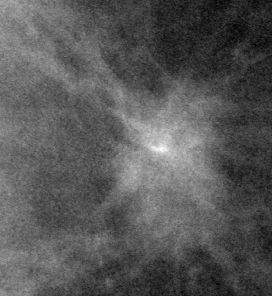
Region of interest cut from a scanned film mammogram (one marked finding); left breast; CC view; BI-RADS breast density category 1 (scale 1–4).
Marked abnormality: mass, shape irregular, margins spiculated; BI-RADS assessment category 5; pathology result (as recorded, not read from the image): malignant.